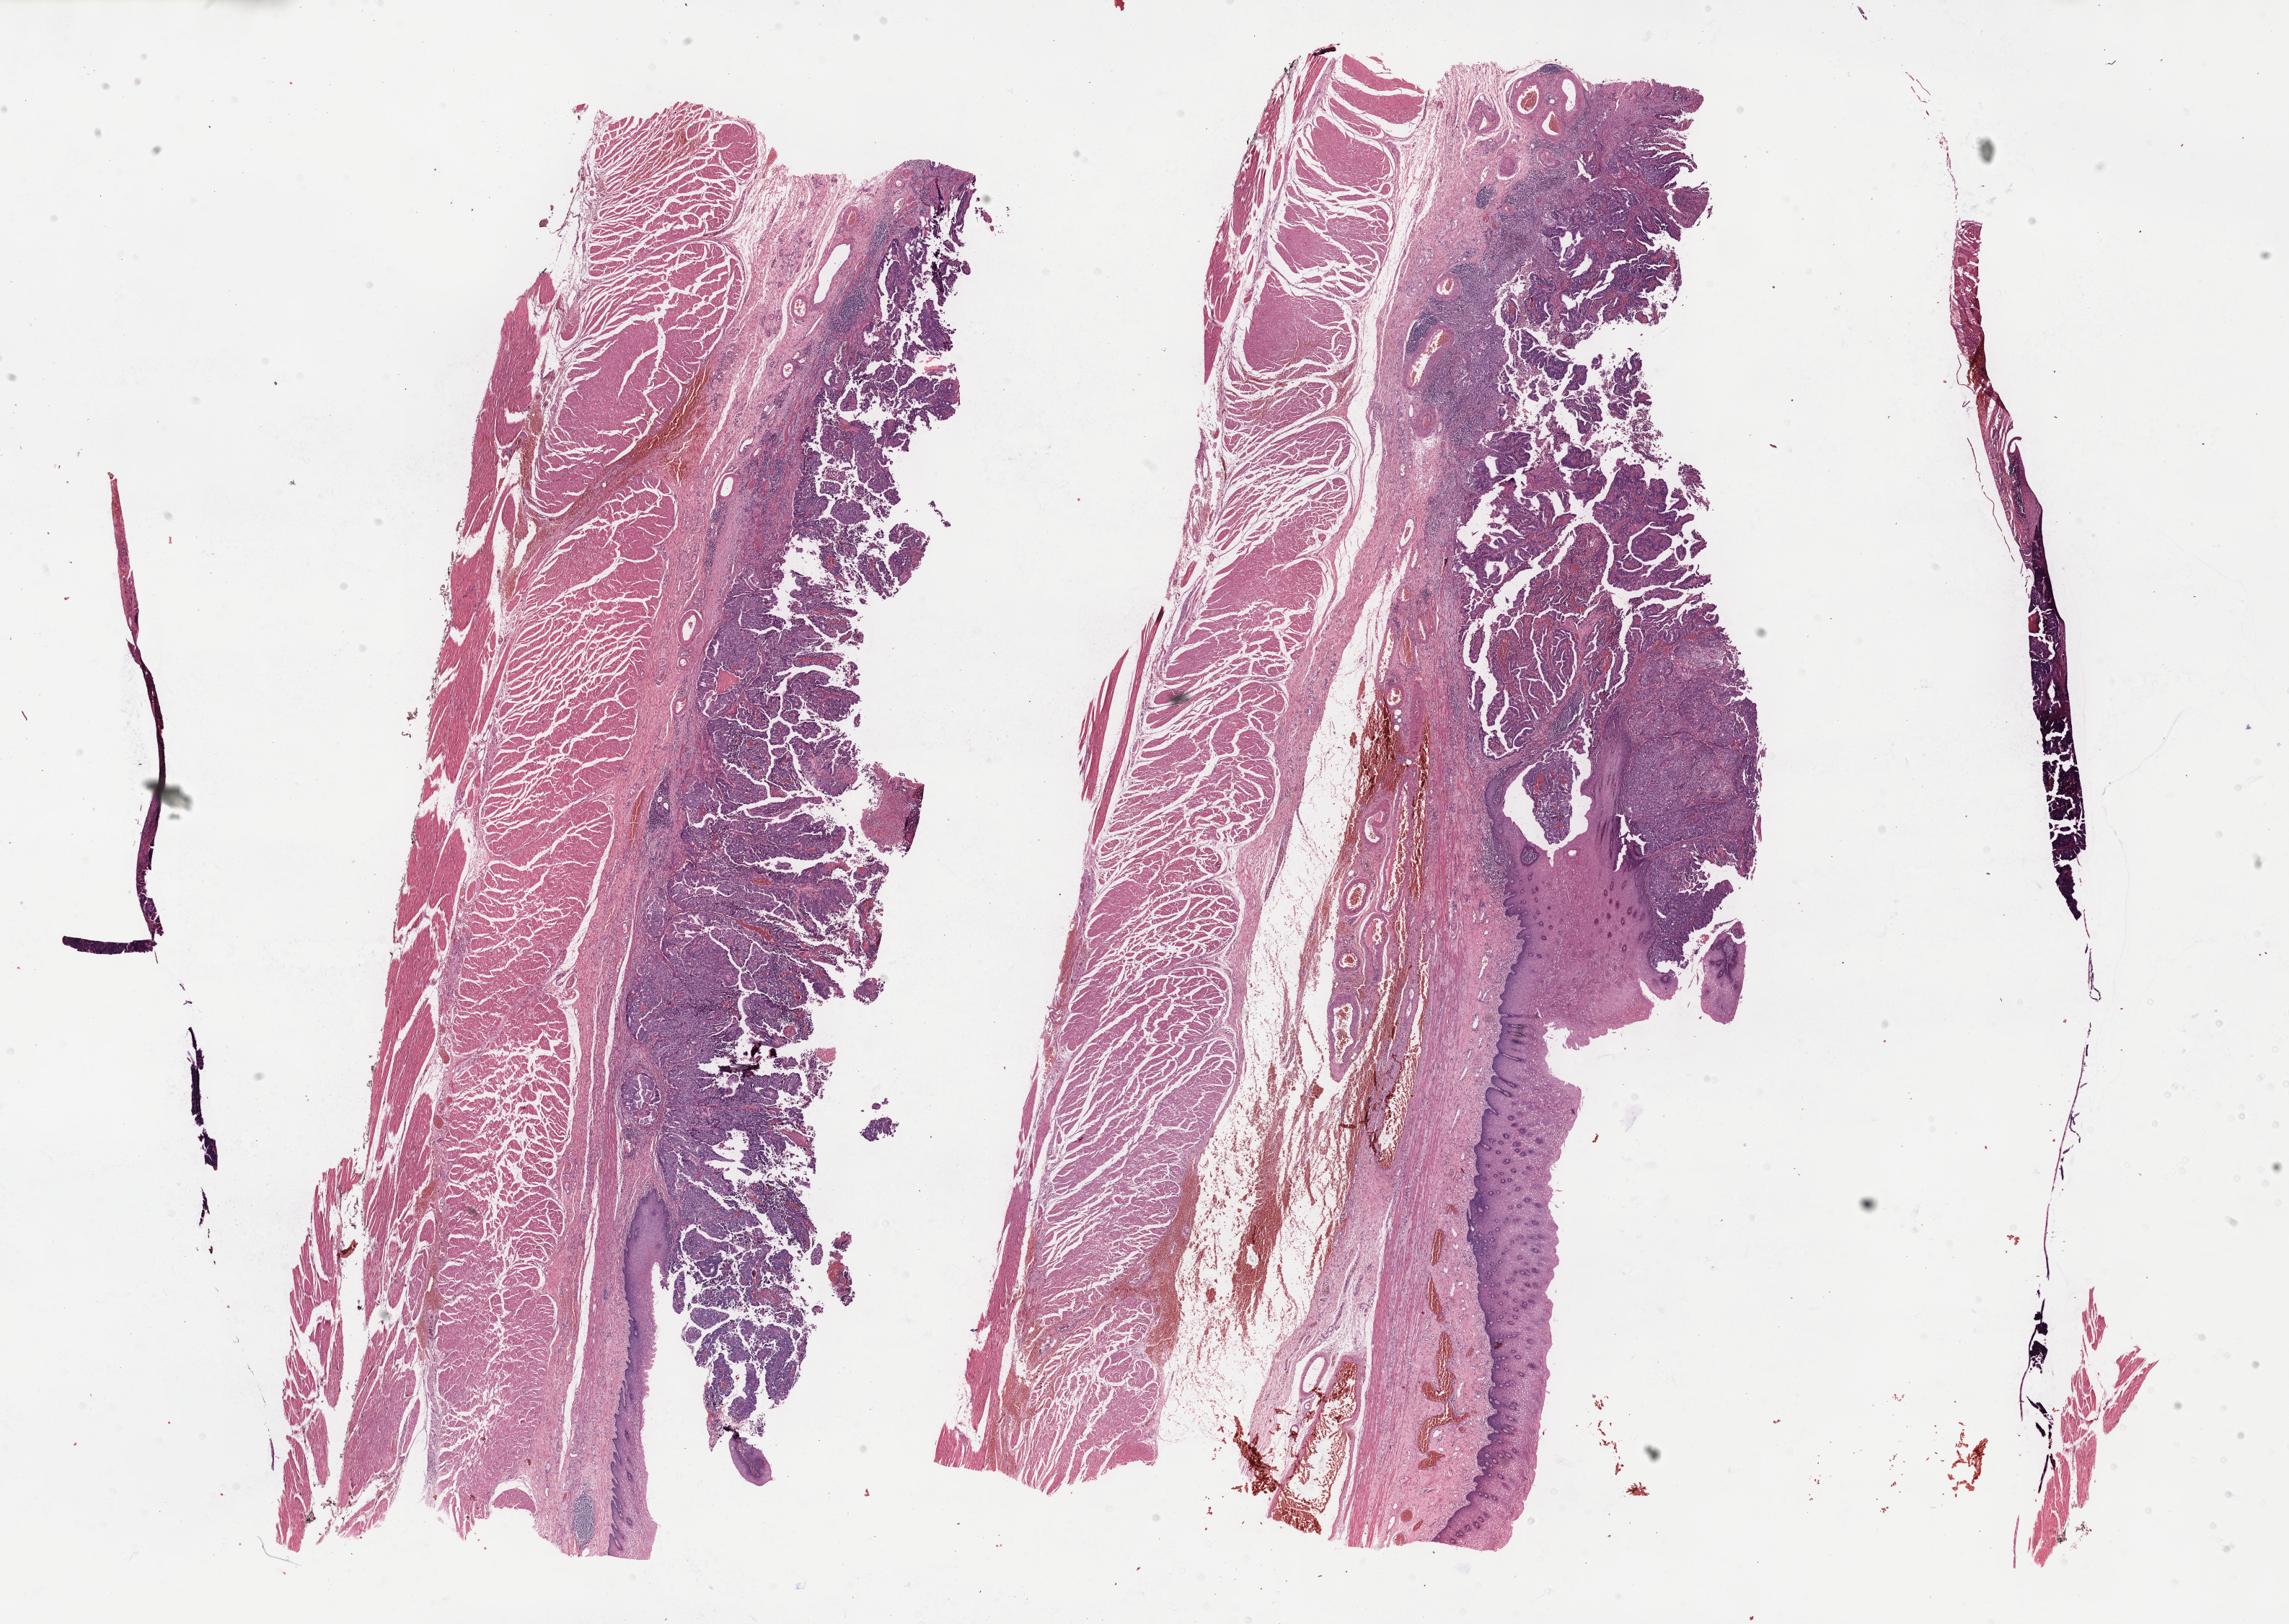
Hematoxylin and eosin (H&E) stained whole-slide image — low-resolution overview of the scanned area, about 25.7 x 18.2 mm; FFPE section; esophagus, primary tumour sample. Male, age 53 years at initial diagnosis. Histologic grade: G2 (moderately differentiated).
• diagnosis: Adenocarcinoma, NOS (lower third of esophagus)
• AJCC pathologic stage: IIB (7th edition)
• lymph nodes positive (case pathology): 6 of 25 examined